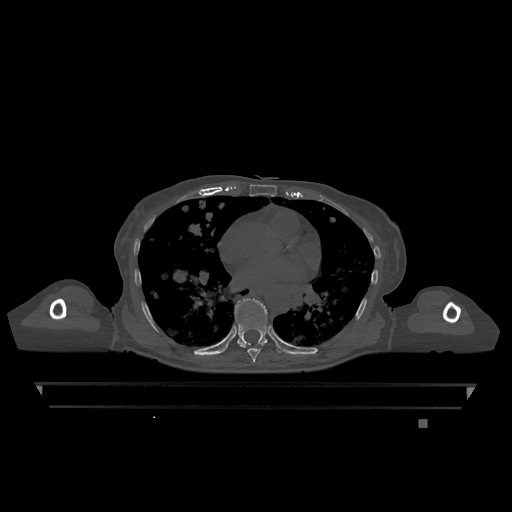
CT including the spine, one axial slice. Slice 713 of 1317 in the series (ordered by position). Bone window (W 1800 / L 400 HU). 0.5 mm slice thickness. 512 × 512 image matrix, field of view 500 × 500 mm. Patient: female, 74 years. Case-level facts recorded for this patient, not image findings: primary cancer: lung; vertebrae with lytic lesions (as recorded): T1, T4, T5, T6, L4, L5.
Outlined on this slice (semi-automatic segmentation, software-assisted and operator-edited):
- T7 vertebra: bounding box (x1, y1, x2, y2) in pixels: (239, 344, 264, 362)
- T9 vertebra: (235, 298, 281, 353)